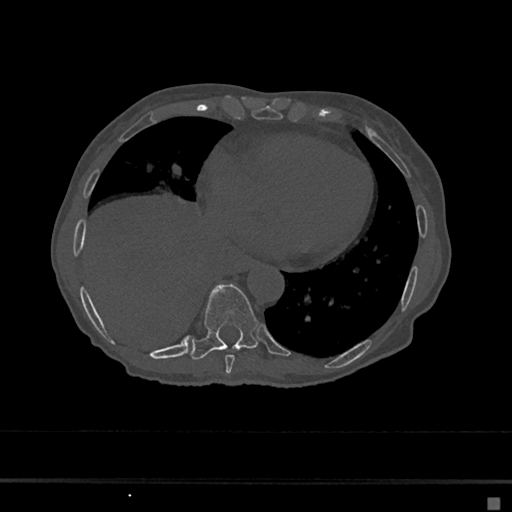
CT including the spine, one axial slice. Position 284 of 797 along the scan axis. 120 kVp. Bone window (W 1800 / L 400 HU). 512 × 512 image matrix. Female patient, age 68 years. Case-level facts recorded for this patient, not image findings: primary cancer: renal.
Annotated regions visible in this slice (semi-automatically segmented with operator editing):
- T8 vertebra: bounding box <225,355,235,374> (left, top, right, bottom; pixels)
- T9 vertebra: <190,284,259,360>